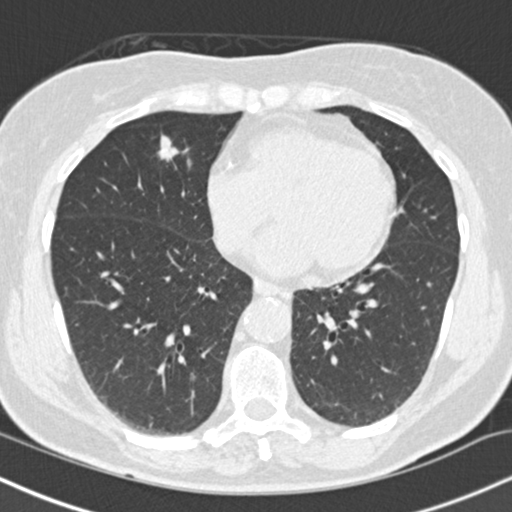
Low-dose screening chest CT, one axial slice; lung window (W 1500 / L -600 HU); 512 × 512 image matrix, field of view 320 × 320 mm.
Structures marked on this image (expert manual segmentation):
- lesion 1 (tumor, middle lobe of right lung): bounding box (x1, y1, x2, y2) in pixels: (158, 135, 179, 162)